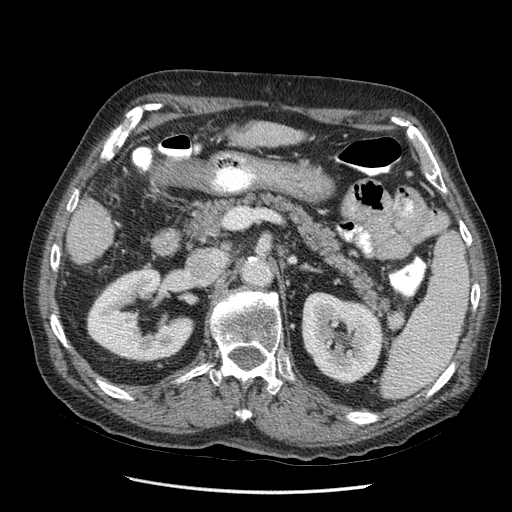
Contrast-enhanced abdominal CT (liver protocol), one axial slice; position 14 of 67 along the scan axis; reconstruction kernel STANDARD; soft-tissue window (W 400 / L 40 HU); 2.5 mm slice thickness; 512 × 512 image matrix, field of view 360 × 360 mm. Case-level facts recorded for this patient, not image findings: diagnosis: hepatocellular carcinoma (patient treated with transarterial chemoembolisation; whether this scan precedes or follows treatment is not stated here); TNM stage (as recorded): Stage-I; Child-Pugh class: A; tumour differentiation: moderately differentiated; tumour nodularity: uninodular.
Outlined on this slice (semi-automatic segmentation, software-assisted and operator-edited):
- liver parenchyma outside the tumour (the mass and vessels are separate outlines, so this box may not span the whole liver): bounding box [x1, y1, x2, y2] px = [210, 118, 312, 155]